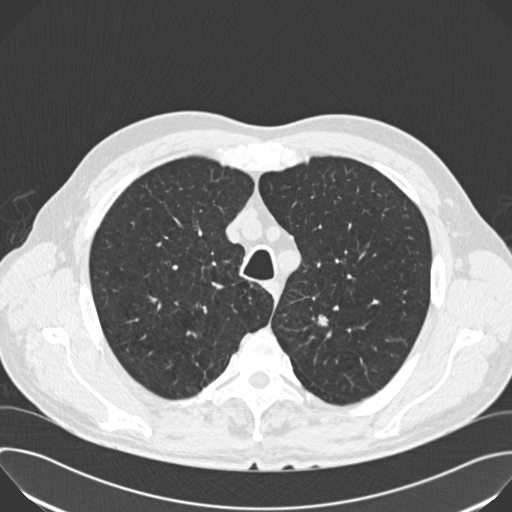
Low-dose screening chest CT, axial slice. Second annual screen. Lung window (W 1500 / L -600 HU). 2 mm slice thickness. Standard (soft-tissue) reconstruction kernel (B30f). 120 kVp. Slice 44 of 200 in the series. 512 × 512 image matrix. Male participant, aged 66 years at enrolment.
Expert reader's lesion annotation, bounding box (x1, y1, x2, y2) in pixels: (303, 302, 345, 342). Reader record for this screening exam (exam-level; its link to the box is not recorded): non-calcified nodule or mass ≥4 mm, left upper lobe, 8 × 7 mm, poorly defined margins, soft tissue attenuation, pre-existing on the prior screen: yes; interval growth: yes. Official screen result: positive, other. Later outcome: lung cancer diagnosed 390 days after this screen (after the third annual screen) — squamous cell carcinoma, NOS, left upper lobe, poorly differentiated (G3), stage IA (AJCC 6th edition), 15 mm at pathology.